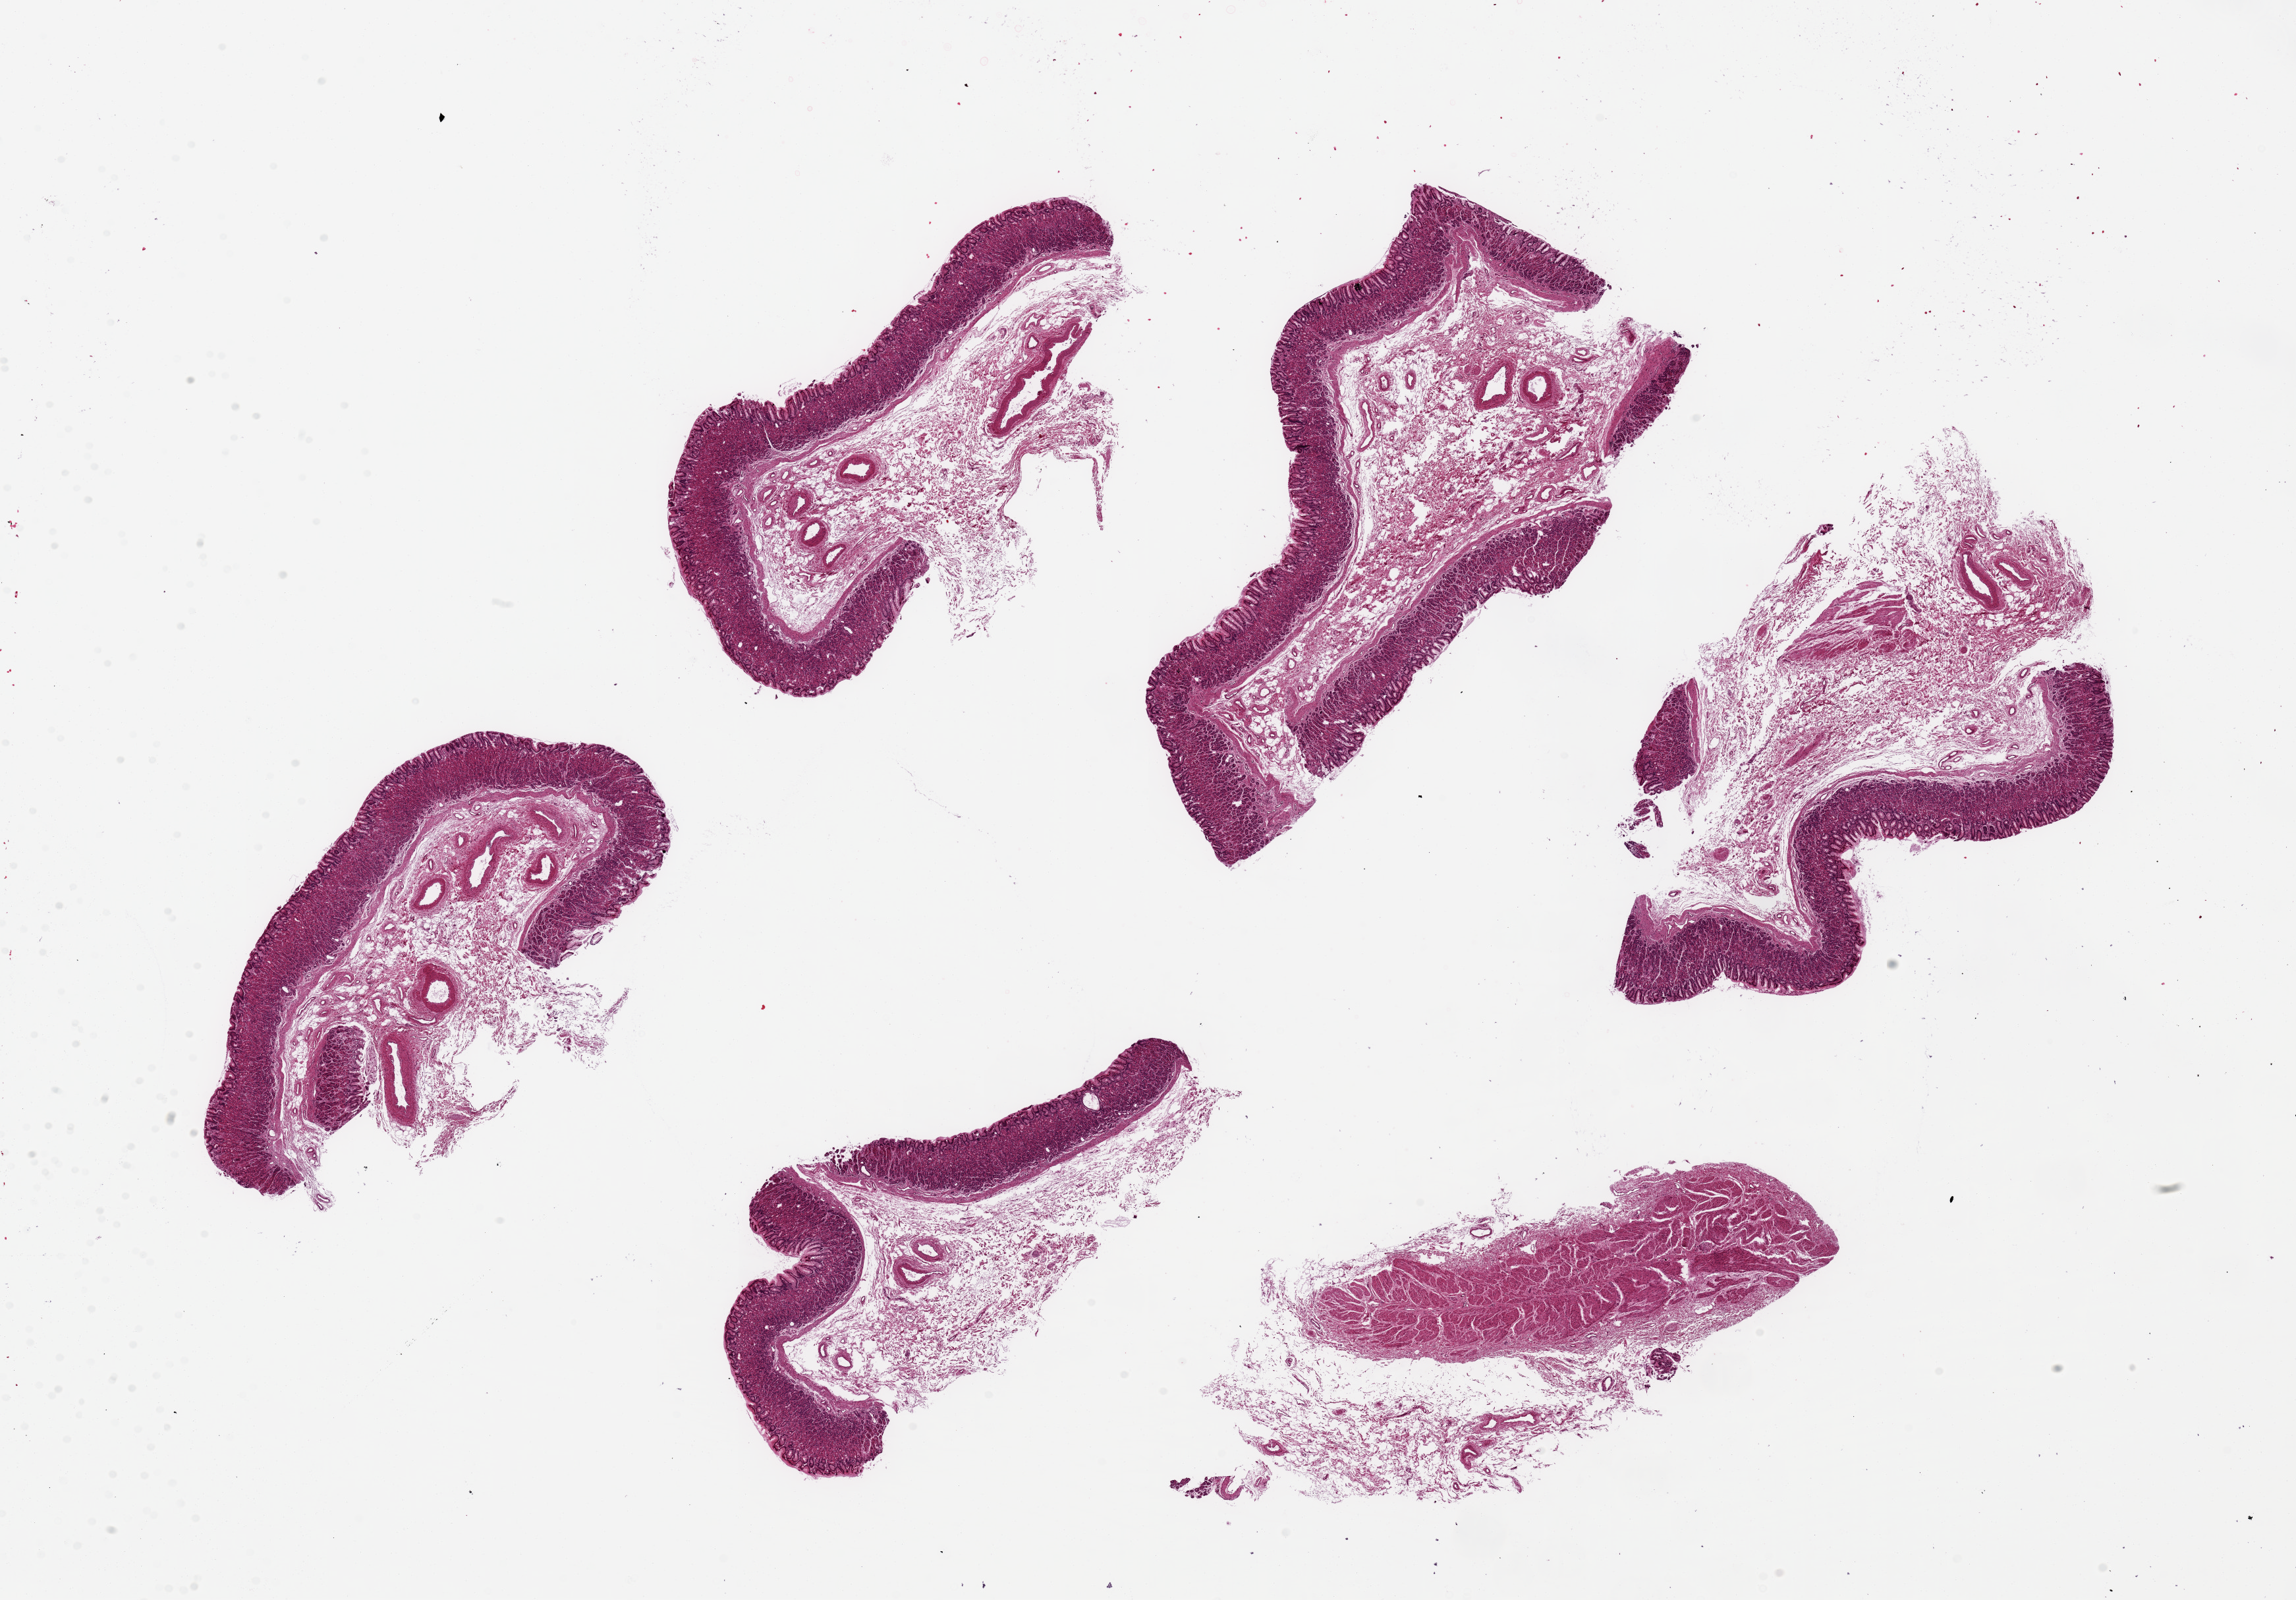
Haematoxylin and eosin whole-slide image — a low-resolution overview of the entire scanned area, about 27.6 x 19.2 mm (slide scanned at 20x), PAXgene-fixed paraffin-embedded (PFPE) section, sampled site (target tissue): stomach, tissue donor sample. Donor: female.
* review note (as recorded): 6 ~7.5x3mm pieces. Mucosa is fairly well preserved, ~20-25% of thickness